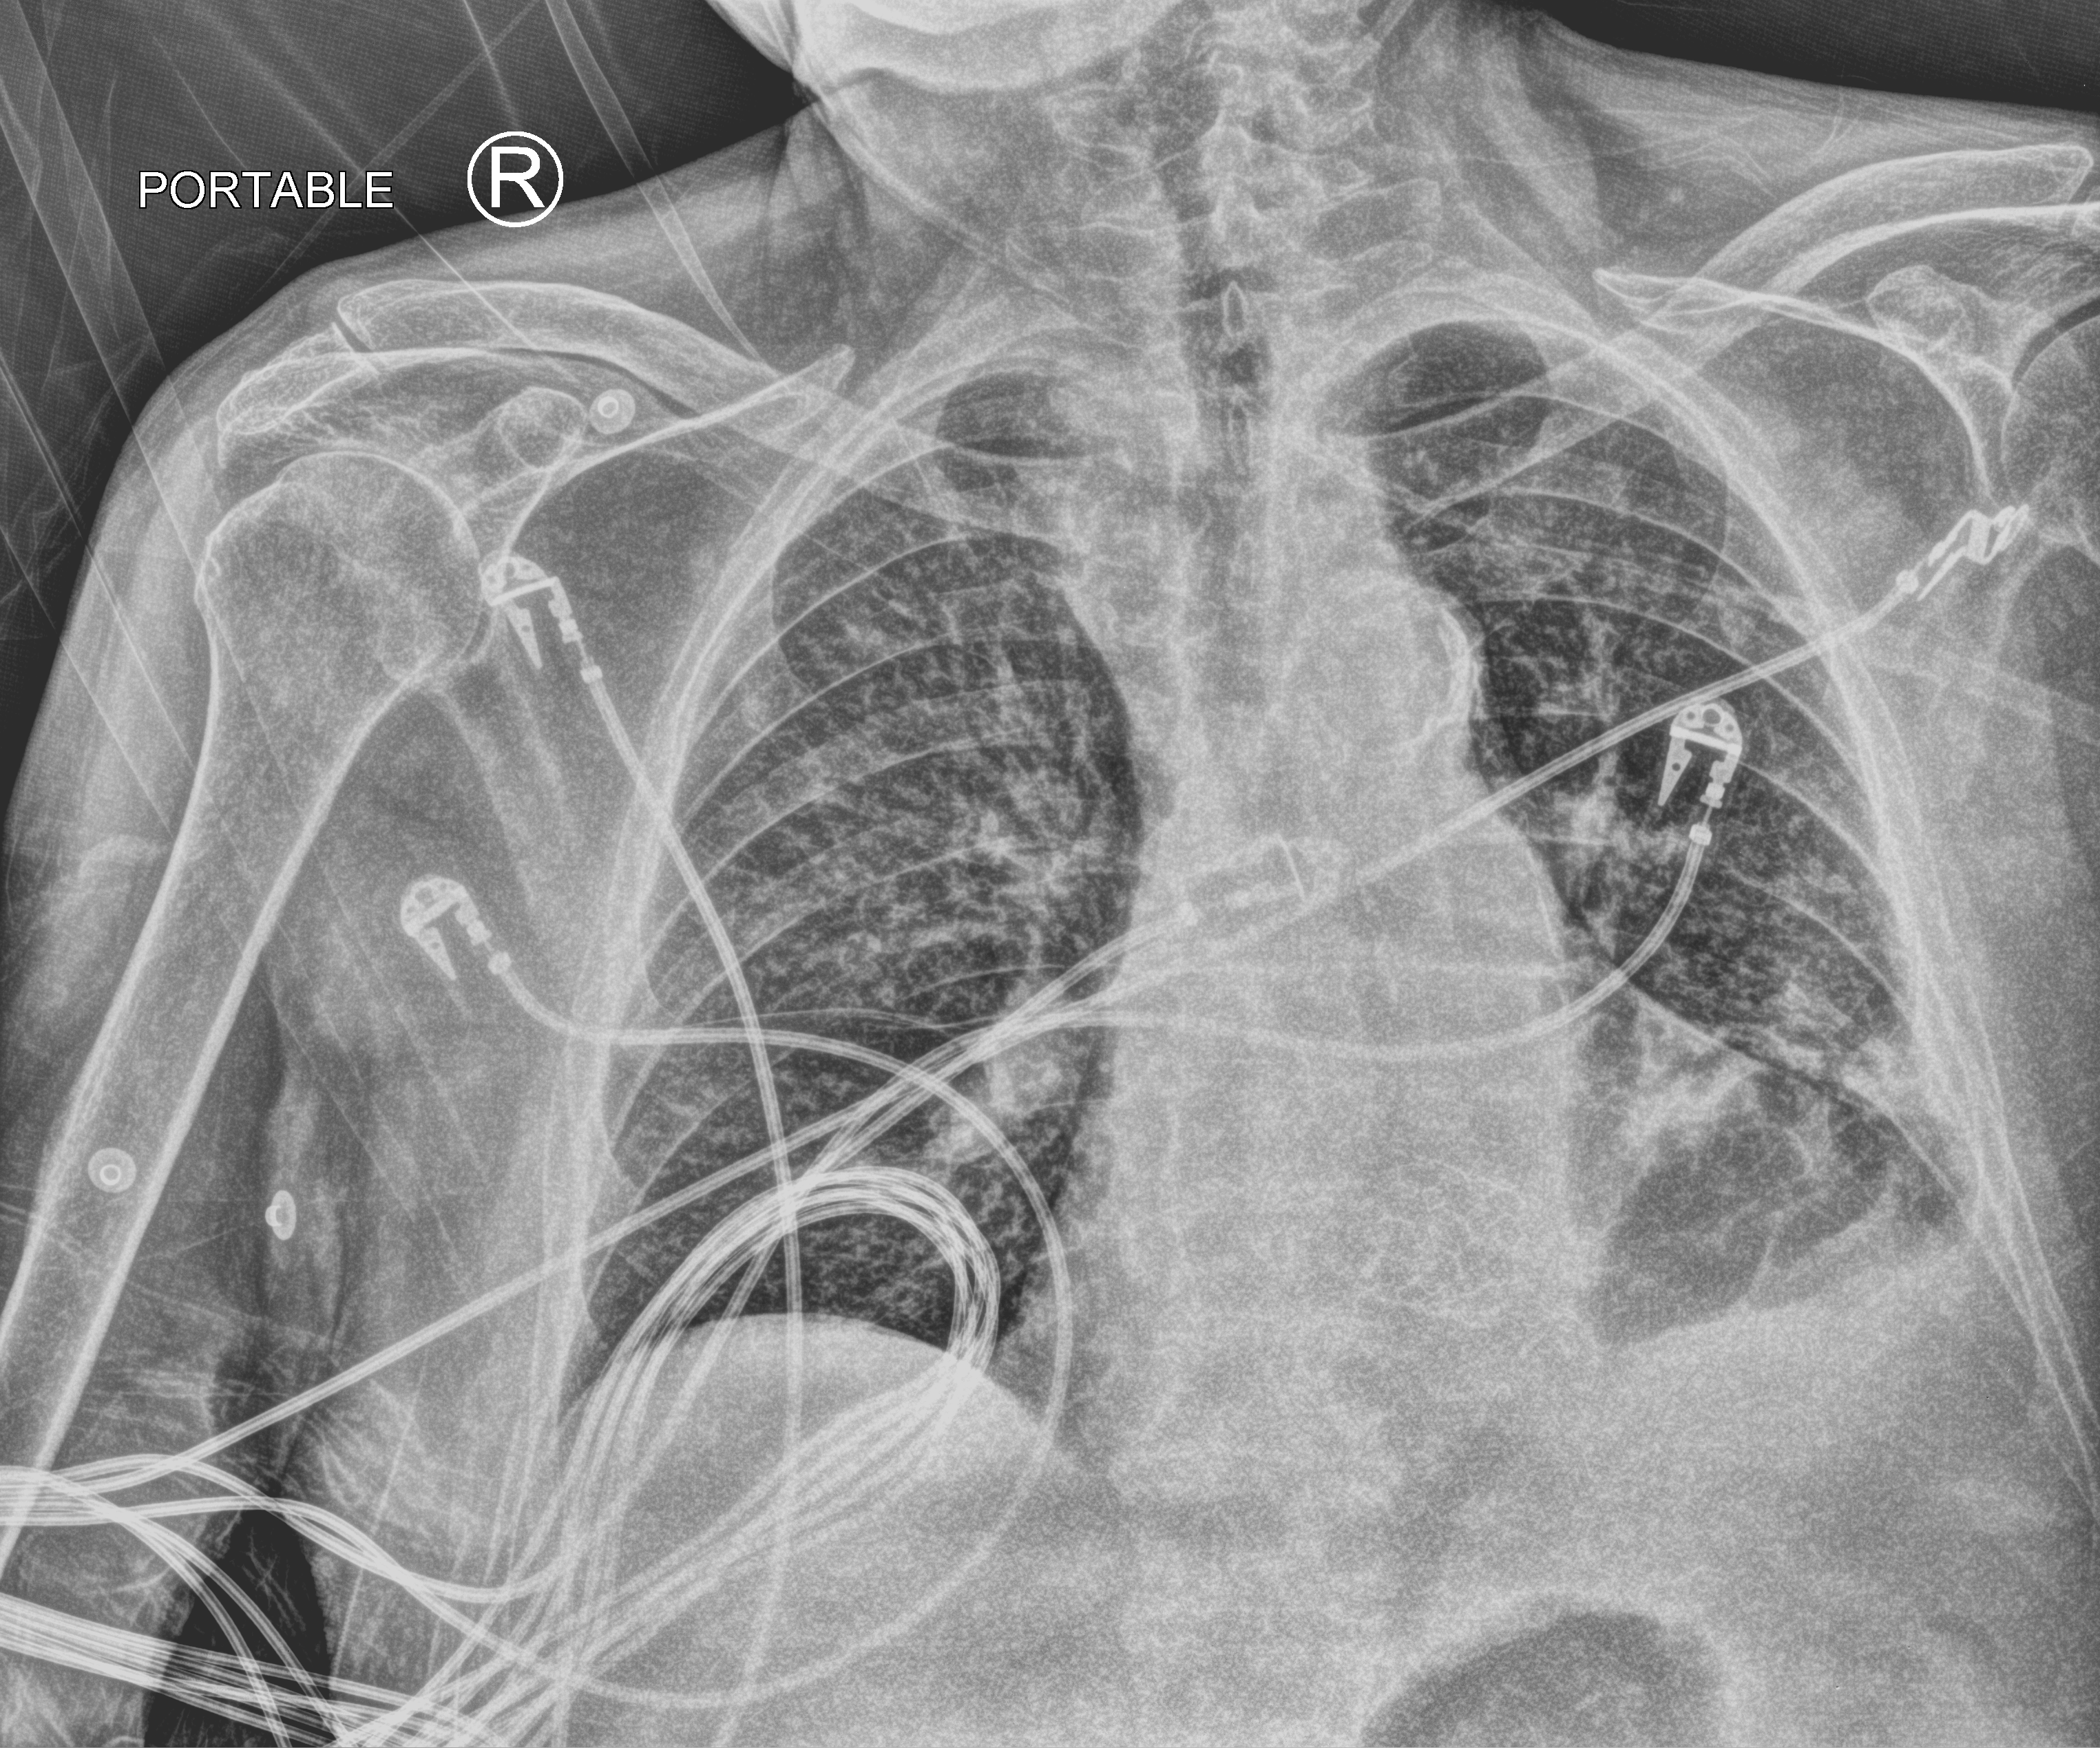
Chest X-ray (portable), anteroposterior (AP) projection. Male patient hospitalised with COVID-19, age 75–90 years.
Hospital-stay facts (about this admission, not read from this image; timing relative to this image not recorded): mechanically ventilated during this hospital stay: no; length of hospital stay: 8 days.